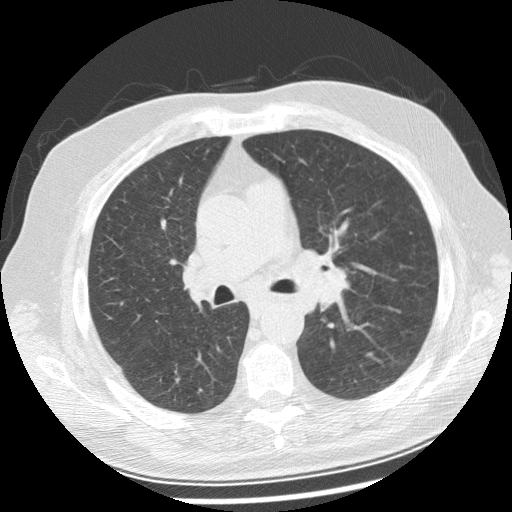
Low-dose screening chest CT, one axial slice; position 149 of 250 along the scan axis; 120 kVp; lung window (W 1500 / L -600 HU); 2.5 mm slice thickness; 512 × 512 image matrix.
Outlined on this slice (manually delineated by an expert):
- lesion 1 (tumor, left main bronchus): bounding box (x1, y1, x2, y2) in pixels: (309, 267, 351, 312)